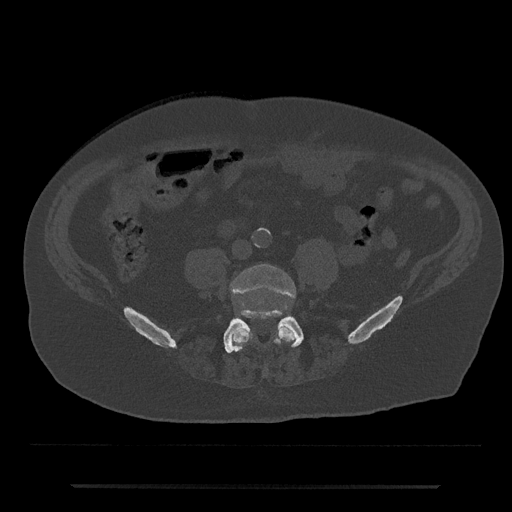
CT including the spine, one axial slice. Position 316 of 797 along the scan axis. Reconstruction kernel Br40s/3. Bone window (W 1800 / L 400 HU). 0.5 mm slice thickness. 512 × 512 image matrix, field of view 434 × 434 mm. Patient: male, 80 years. From the clinical record (not read from this slice): primary cancer: prostate; vertebrae with lytic lesions (as recorded): L1, T11.
Outlined on this slice (semi-automatically segmented with operator editing):
- L4 vertebra: box from (x=230, y=264) to (x=296, y=349) px
- L5 vertebra: (x=223, y=310)–(x=304, y=353)